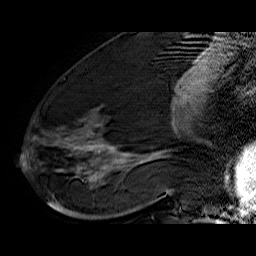
Breast MRI (dynamic contrast-enhanced), one sagittal slice; position 28 of 60 along the scan axis; dynamic contrast-enhanced series, time point 2 of 6 at this slice position (early post-contrast); 1.5 T; TE 6.4 ms, TR 32.9 ms; 256 × 256 image matrix. Female patient. From the clinical record (not read from this slice): setting: breast cancer imaged before/during neoadjuvant chemotherapy; receptor status: HR-positive, HER2-negative.
Outlined on this slice (semi-automatic segmentation, software-assisted and operator-edited):
- analysis volume of interest (the breast-tissue region the enhancement analysis was run in; not a lesion): box from (x=40, y=74) to (x=176, y=210) px
- tumour enhancement mask (voxels above the 100 % enhancement threshold inside the analysis volume of interest): (x=69, y=98)–(x=176, y=179)